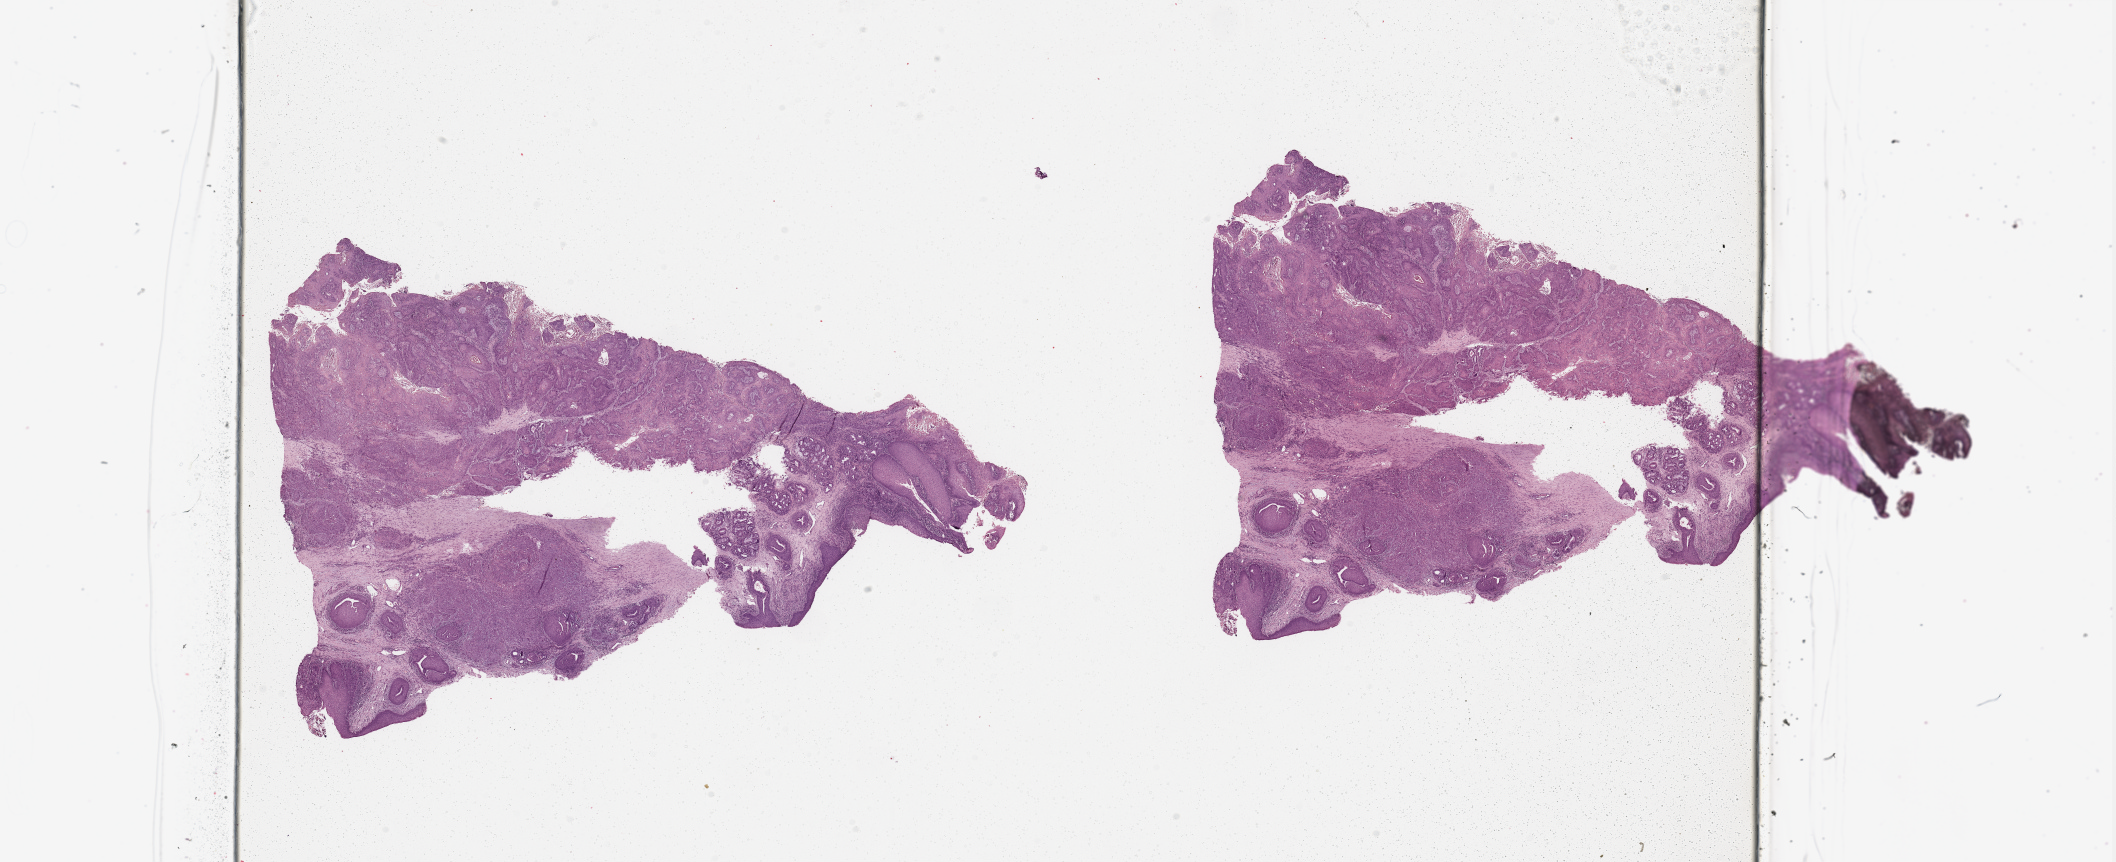
Digitized H&E tissue section (whole slide), a low-resolution overview of the entire scanned area, about 33.5 x 13.6 mm (from a 20x scan); tumour tissue sample, sampled site: larynx. Patient: male, age 58 years. Histologic grade: G2 (moderately differentiated). Slide review estimates, as recorded: tumour nuclei 80%, necrosis 5%.
* primary tumour site (as recorded): larynx
* AJCC pathologic stage: III
* diagnosis: Squamous cell carcinoma, NOS (larynx, NOS)